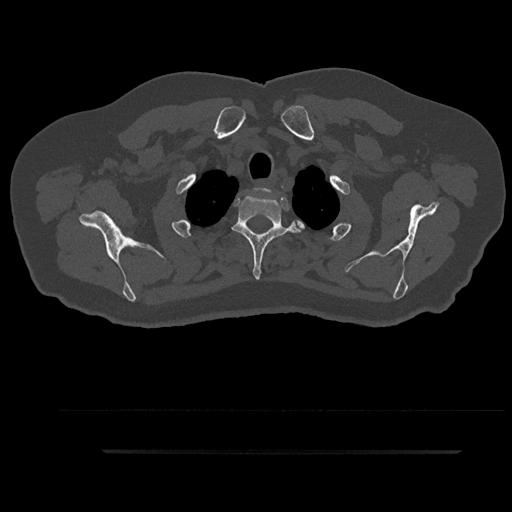
CT including the spine, one axial slice; position 756 of 797 along the scan axis; reconstruction kernel Br40s/3; 120 kVp; bone window (W 1800 / L 400 HU); 512 × 512 image matrix, field of view 432 × 432 mm. Patient: male, 63 years. Case-level facts recorded for this patient, not image findings: primary cancer: renal; vertebrae with lytic lesions (as recorded): T8.
Structures marked on this image (semi-automatically segmented with operator editing):
- T1 vertebra: bounding box <282,206,284,208> (left, top, right, bottom; pixels)
- T2 vertebra: <232,195,304,279>
- T3 vertebra: <219,224,295,249>